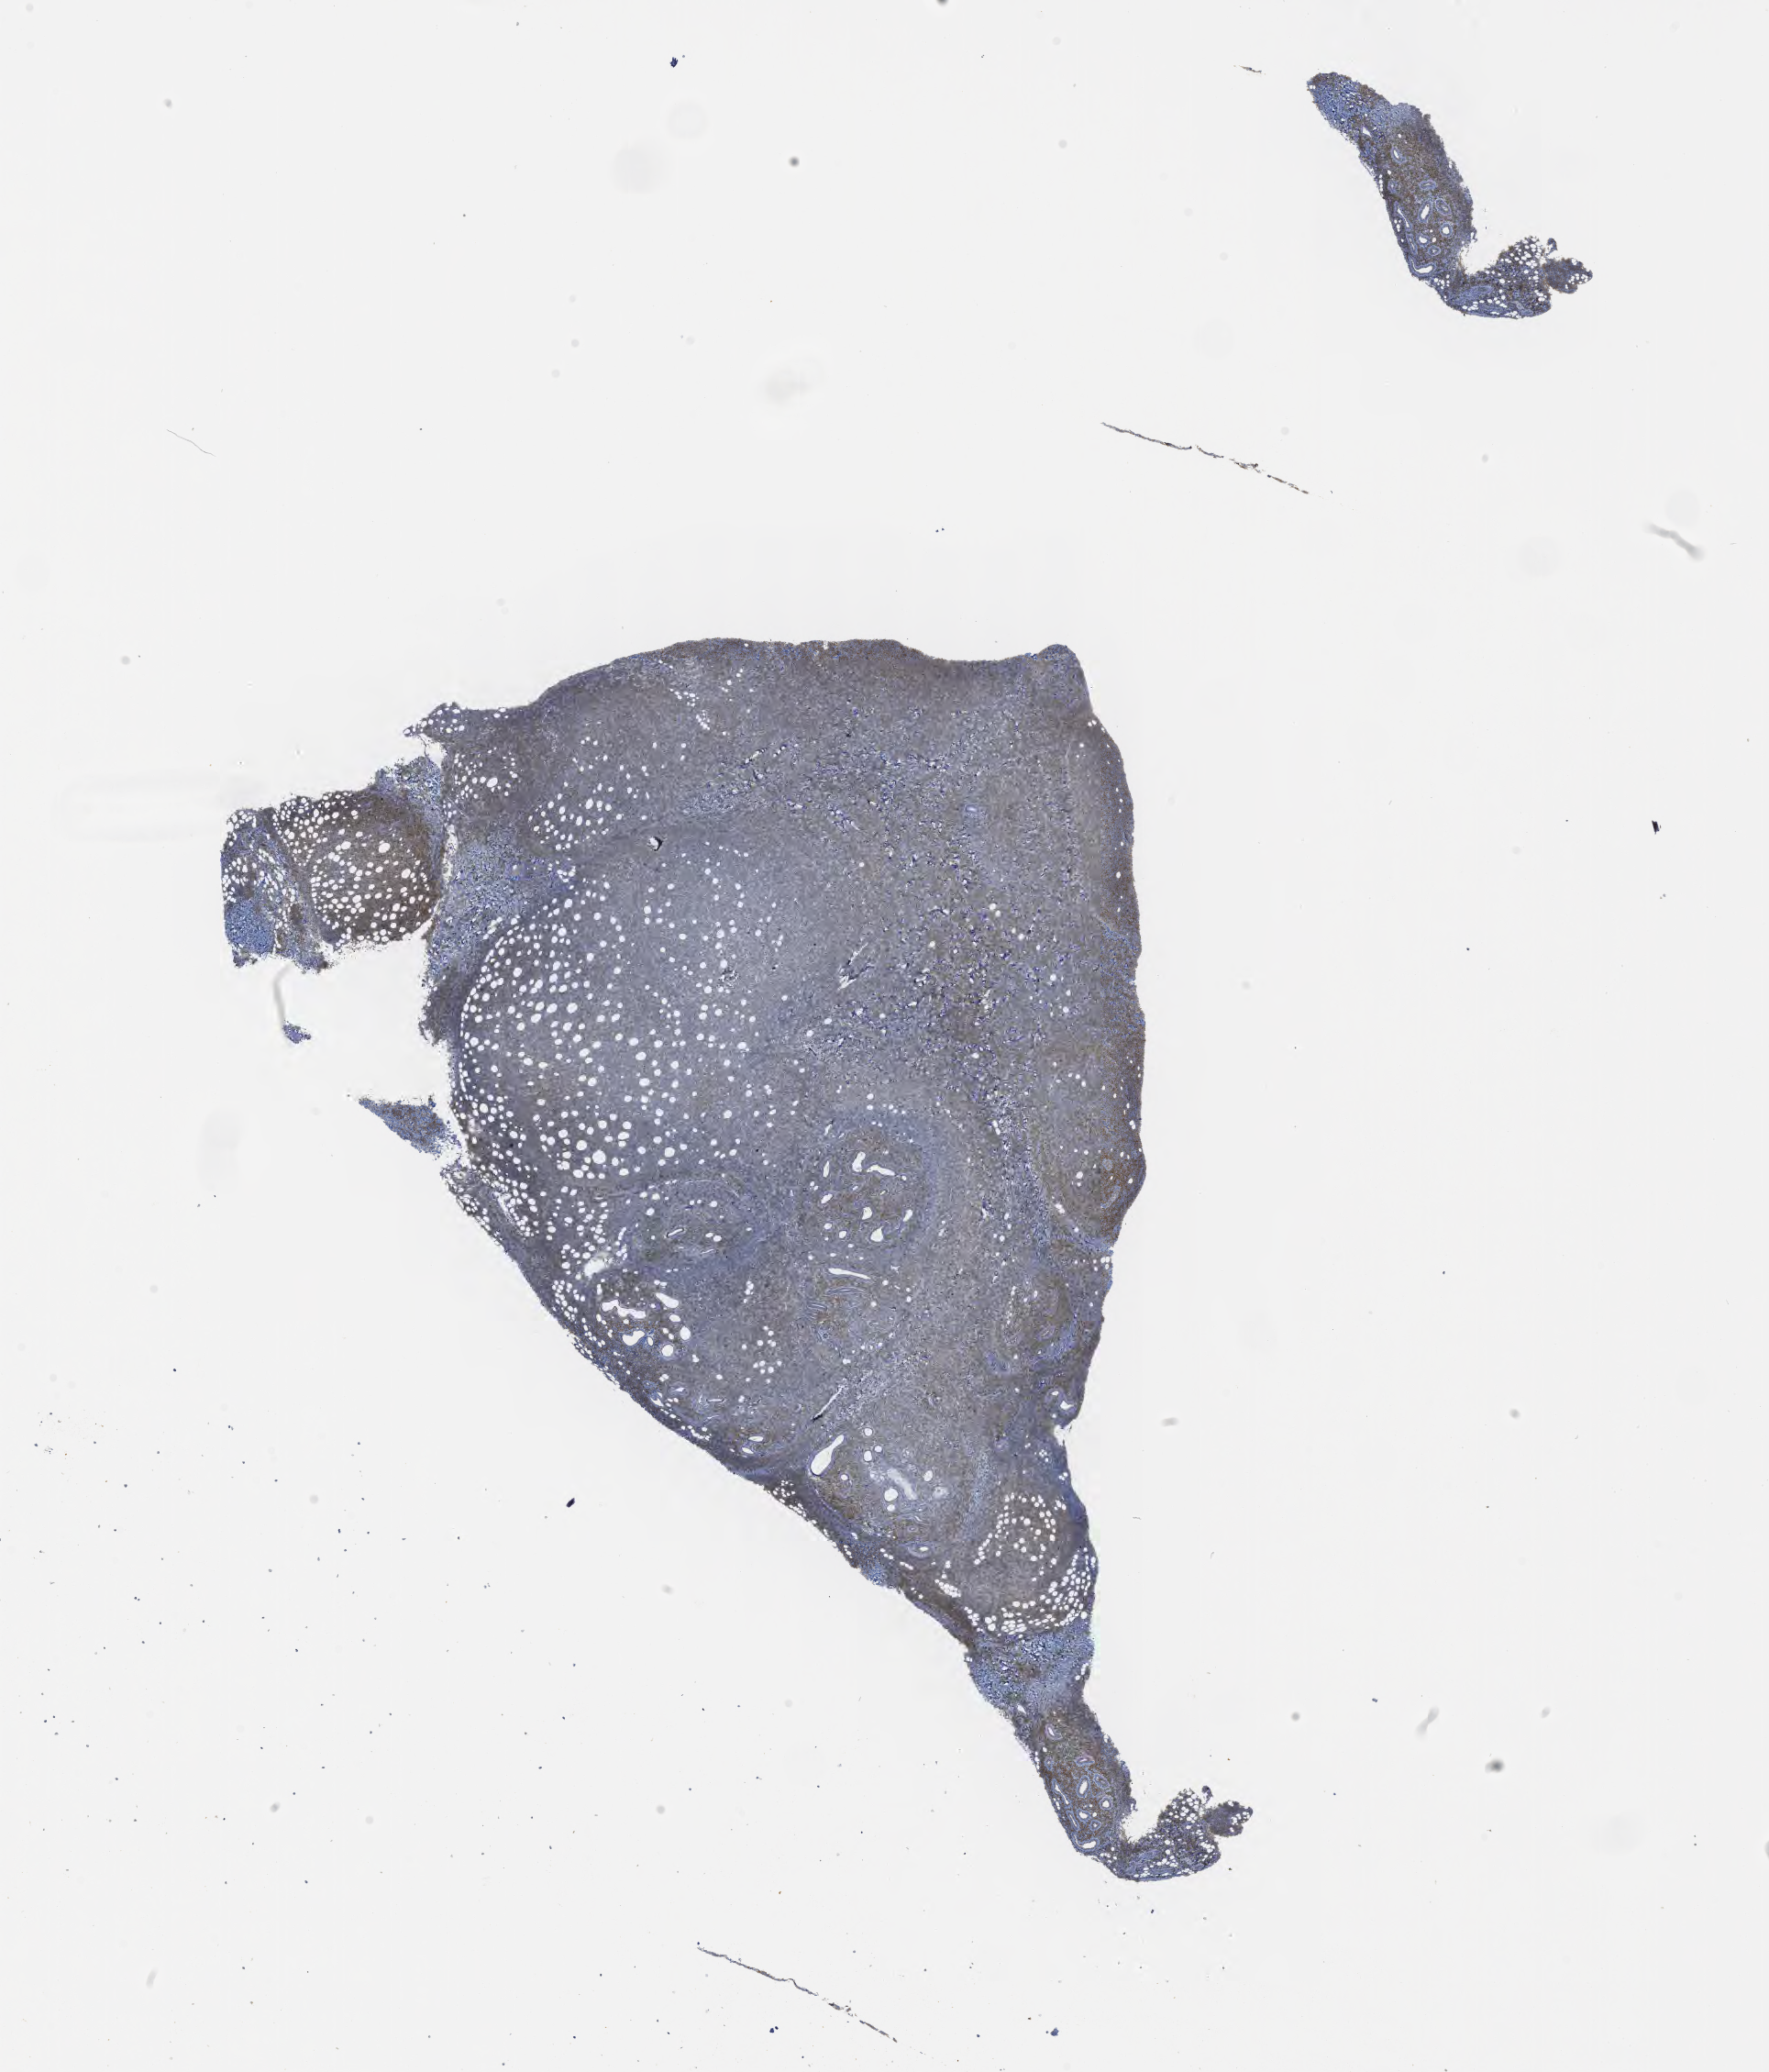
Whole-slide image, immunohistochemical stain for BCL6, a low-resolution overview of the entire scanned area, about 15.6 x 18.3 mm; specimen: tumor tissue. Patient male; aged 46.
Diagnosis: Burkitt lymphoma, NOS.